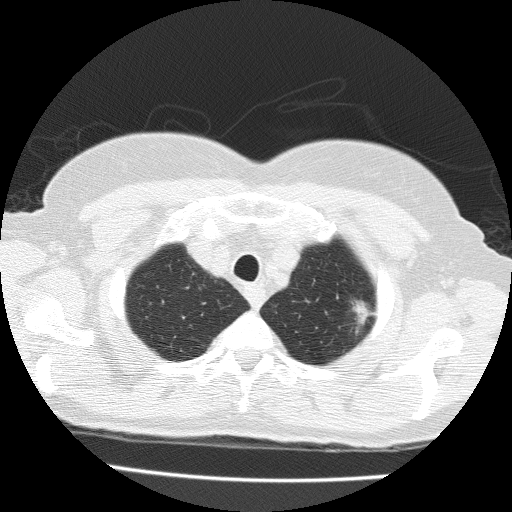
Axial slice from a low-dose chest CT screening exam, baseline screening round, lung window (W 1500 / L -600 HU), 2 mm slice thickness, lung (sharp) reconstruction kernel (FC51). Female participant, aged 71 years at enrolment. Former smoker at enrolment.
Lesion marked by an expert reader, bounding box <339,292,386,334> (left, top, right, bottom; pixels). Screening reader's record for this exam (one nodule recorded; not confirmed to be the boxed lesion): non-calcified nodule or mass ≥4 mm, left upper lobe, 15 × 10 mm, spiculated (stellate) margins, soft tissue attenuation. Later outcome: lung cancer diagnosed 49 days after this screen — adenocarcinoma with mixed subtypes, left upper lobe, well differentiated (G1), stage IA (AJCC 6th edition), 15 mm at pathology.